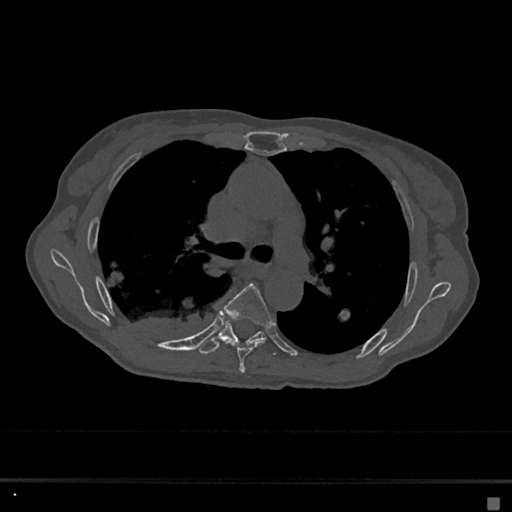
CT including the spine, one axial slice. Reconstruction kernel Br40s/3. 120 kVp. Bone window (W 1800 / L 400 HU). 0.5 mm slice thickness. 512 × 512 image matrix, field of view 360 × 360 mm. Patient: female, 68 years. From the clinical record (not read from this slice): primary cancer: renal.
Annotated regions visible in this slice (semi-automatic segmentation, software-assisted and operator-edited):
- T5 vertebra: bounding box <224,283,272,374> (left, top, right, bottom; pixels)
- T6 vertebra: <197,321,276,355>